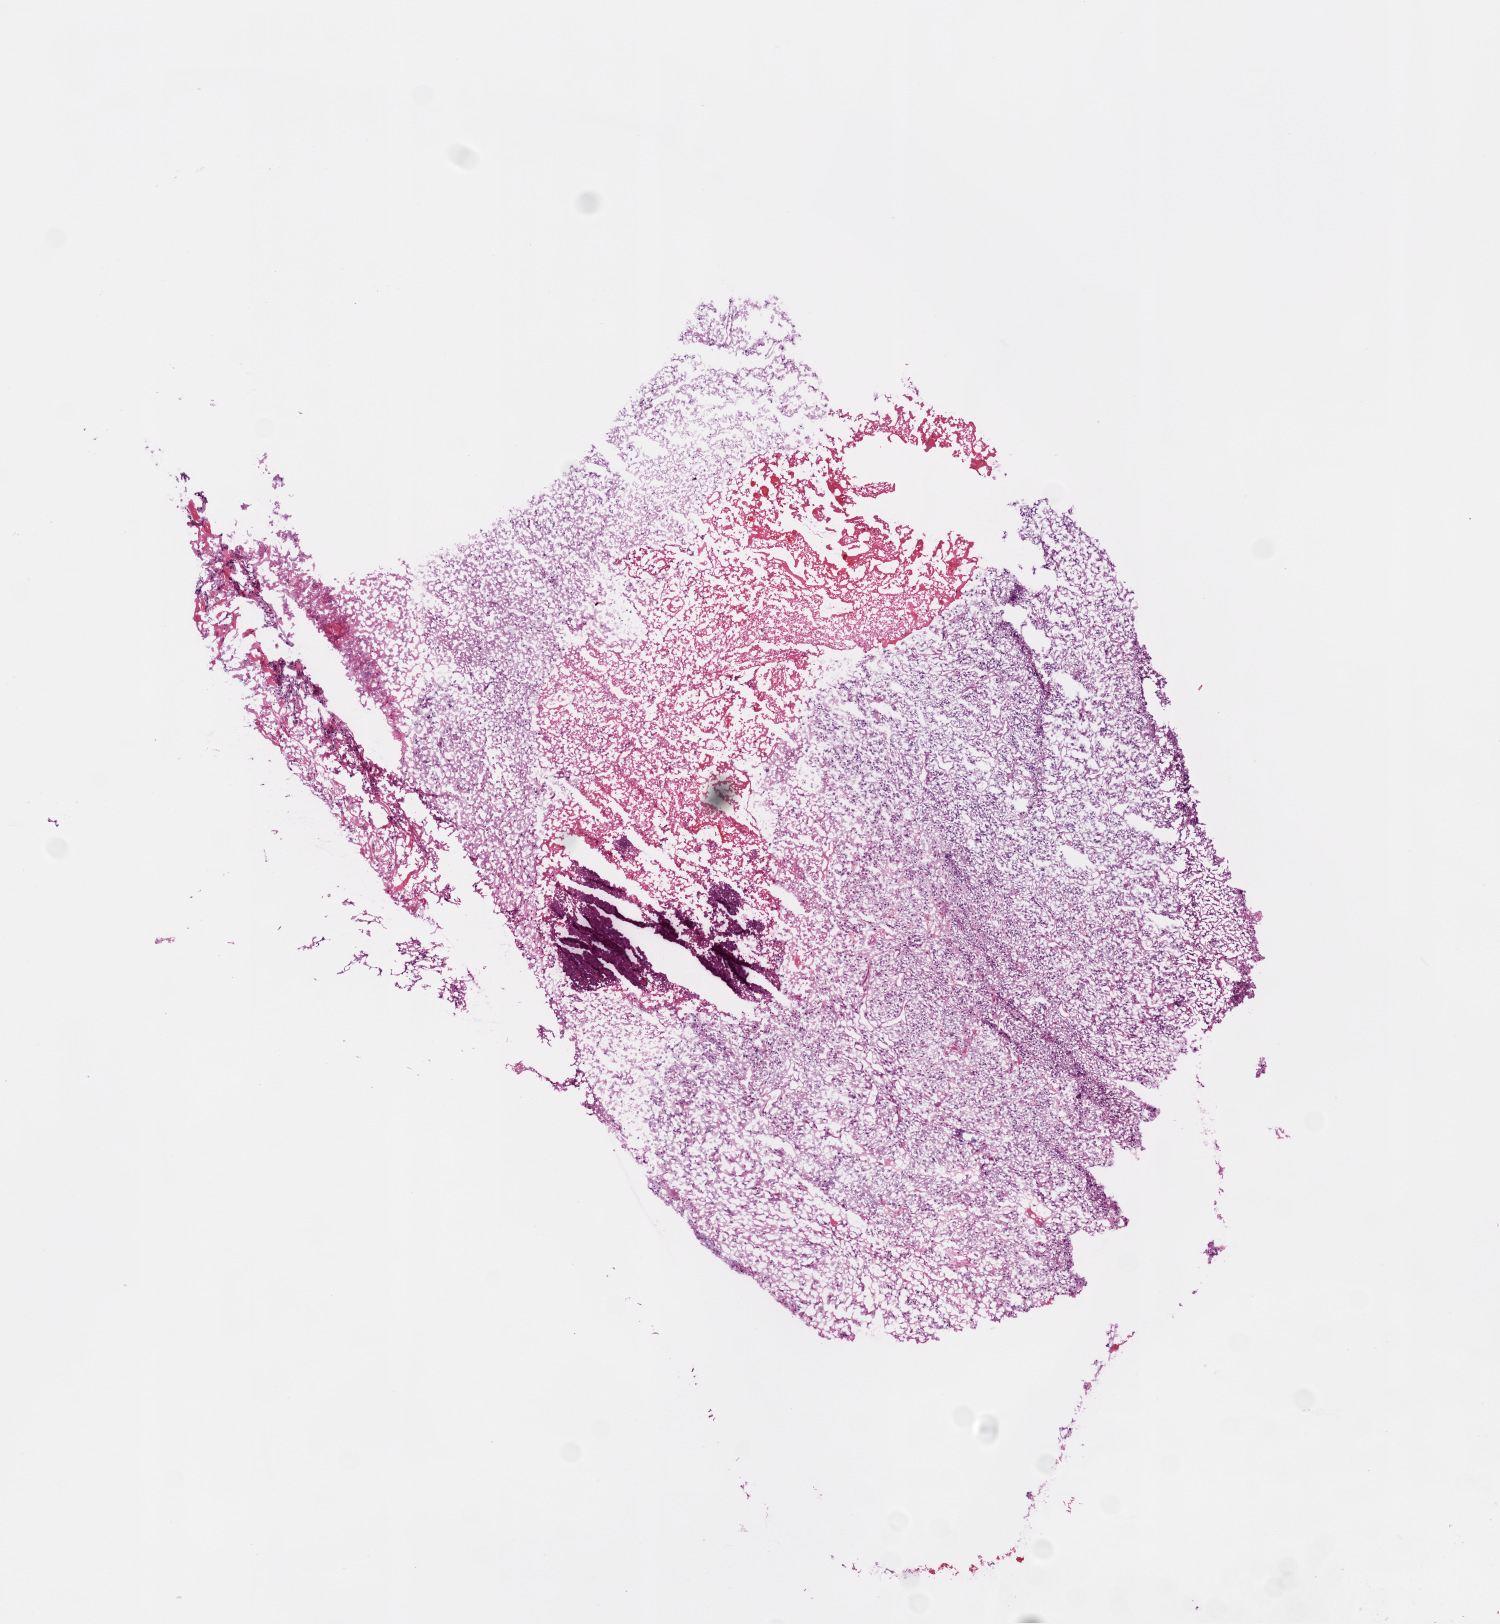
Digitized Hematoxylin and eosin (H&E) stained tissue section (whole slide), whole scanned area (about 6.0 x 6.5 mm, slide scanned at 20x) shown as a low-resolution overview; frozen section from the bottom of the tissue portion; sample: primary tumour, brain. Female patient; age at initial diagnosis 57 years. Composition of this section per pathologist review: tumour cells 100%, tumour nuclei 80%, normal cells 0%, stromal cells 0%, necrosis 0%.
Pathologic diagnosis: Glioblastoma.